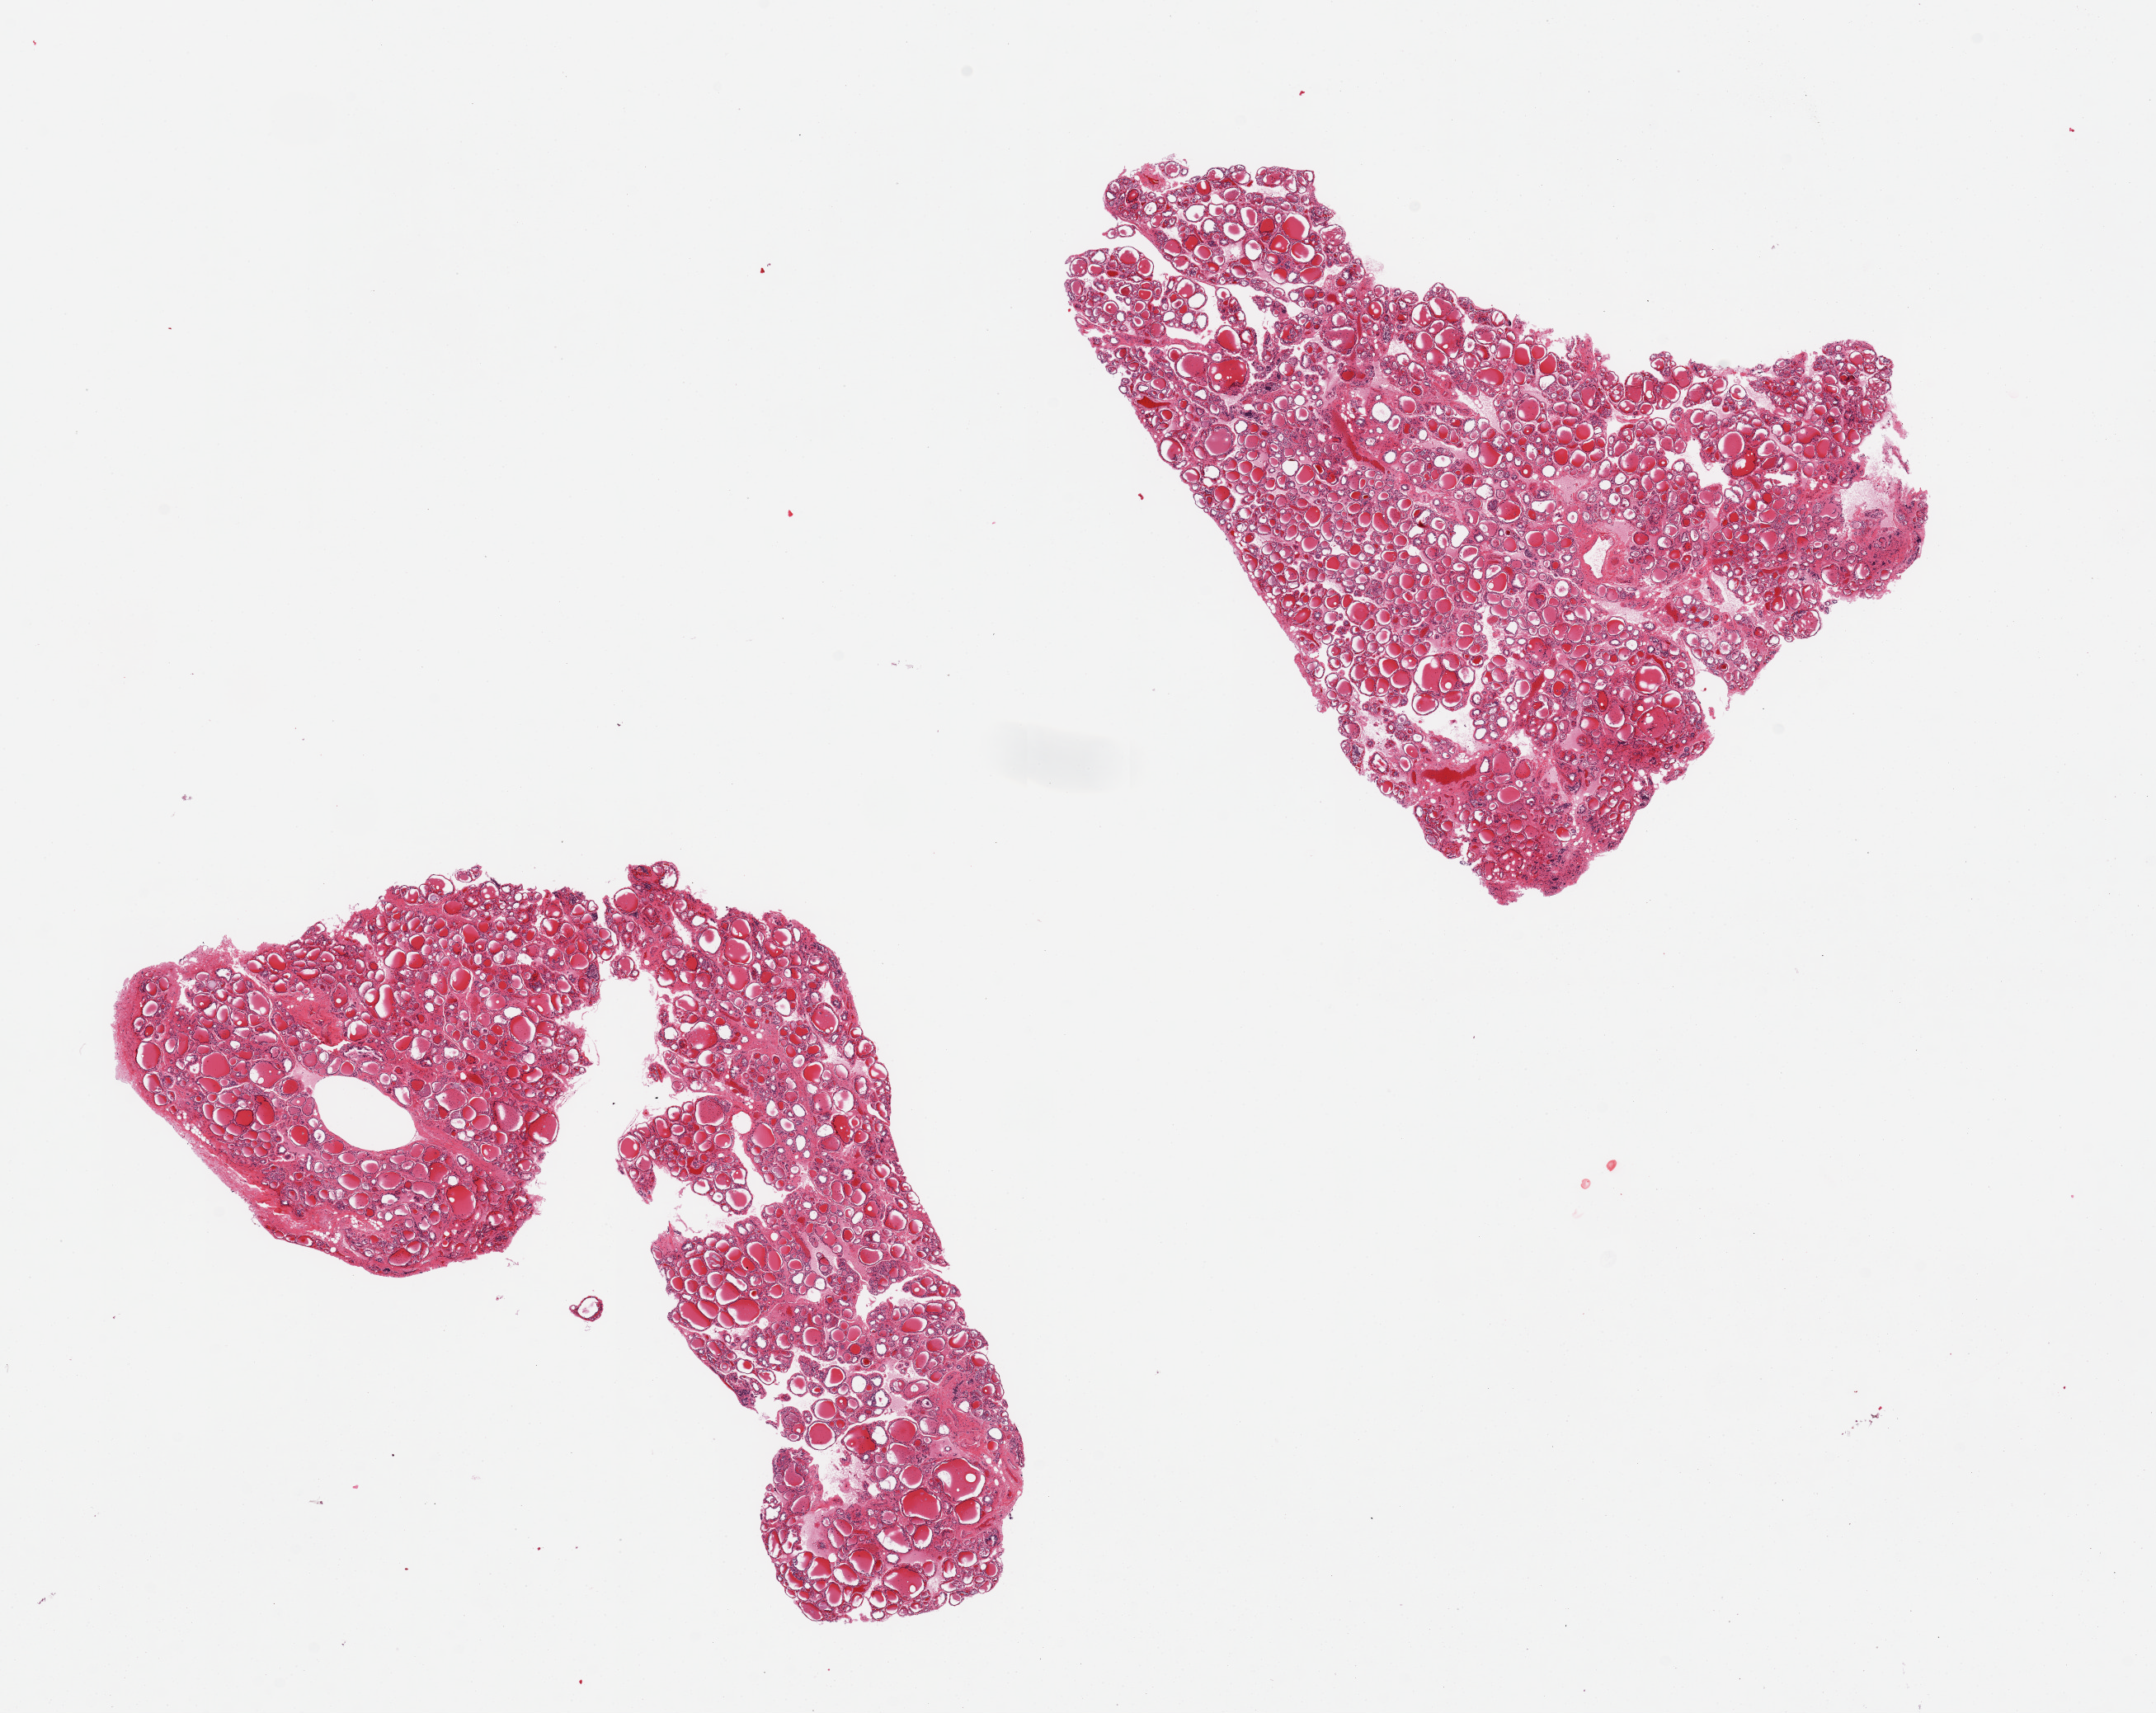
Digitized haematoxylin and eosin-stained section, brightfield, low-resolution overview of the scanned area, about 20.7 x 16.4 mm (from a 20x scan); PAXgene-fixed, paraffin-embedded tissue; target tissue: thyroid; tissue donor sample. Donor: female.
• reviewer comment on this tissue sample: 2 pieces, no significant findings